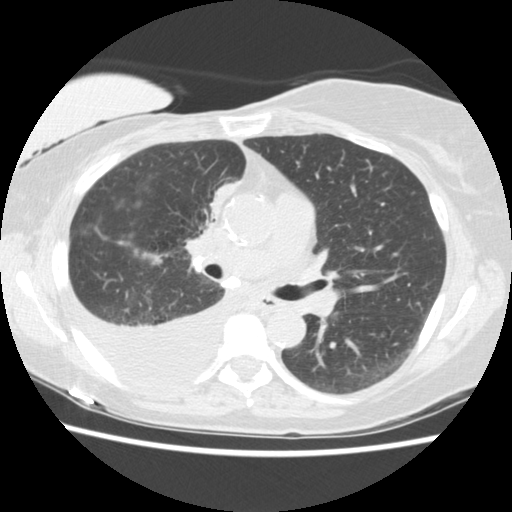
Low-dose screening chest CT, axial slice; third screening round (two years after baseline); lung window (W 1500 / L -600 HU); standard (soft-tissue) reconstruction kernel (STANDARD); slice 71 of 157 in the series; 512 × 512 image matrix, field of view 330 × 330 mm. Female, age 56 years at enrolment.
Expert reader's lesion annotation, box from (x=184, y=170) to (x=249, y=237) px. The screening reader recorded 2 non-calcified nodules or masses ≥4 mm on this exam (right middle lobe, right lower lobe); which of them this box marks is not recorded. Official screen result: positive, other.